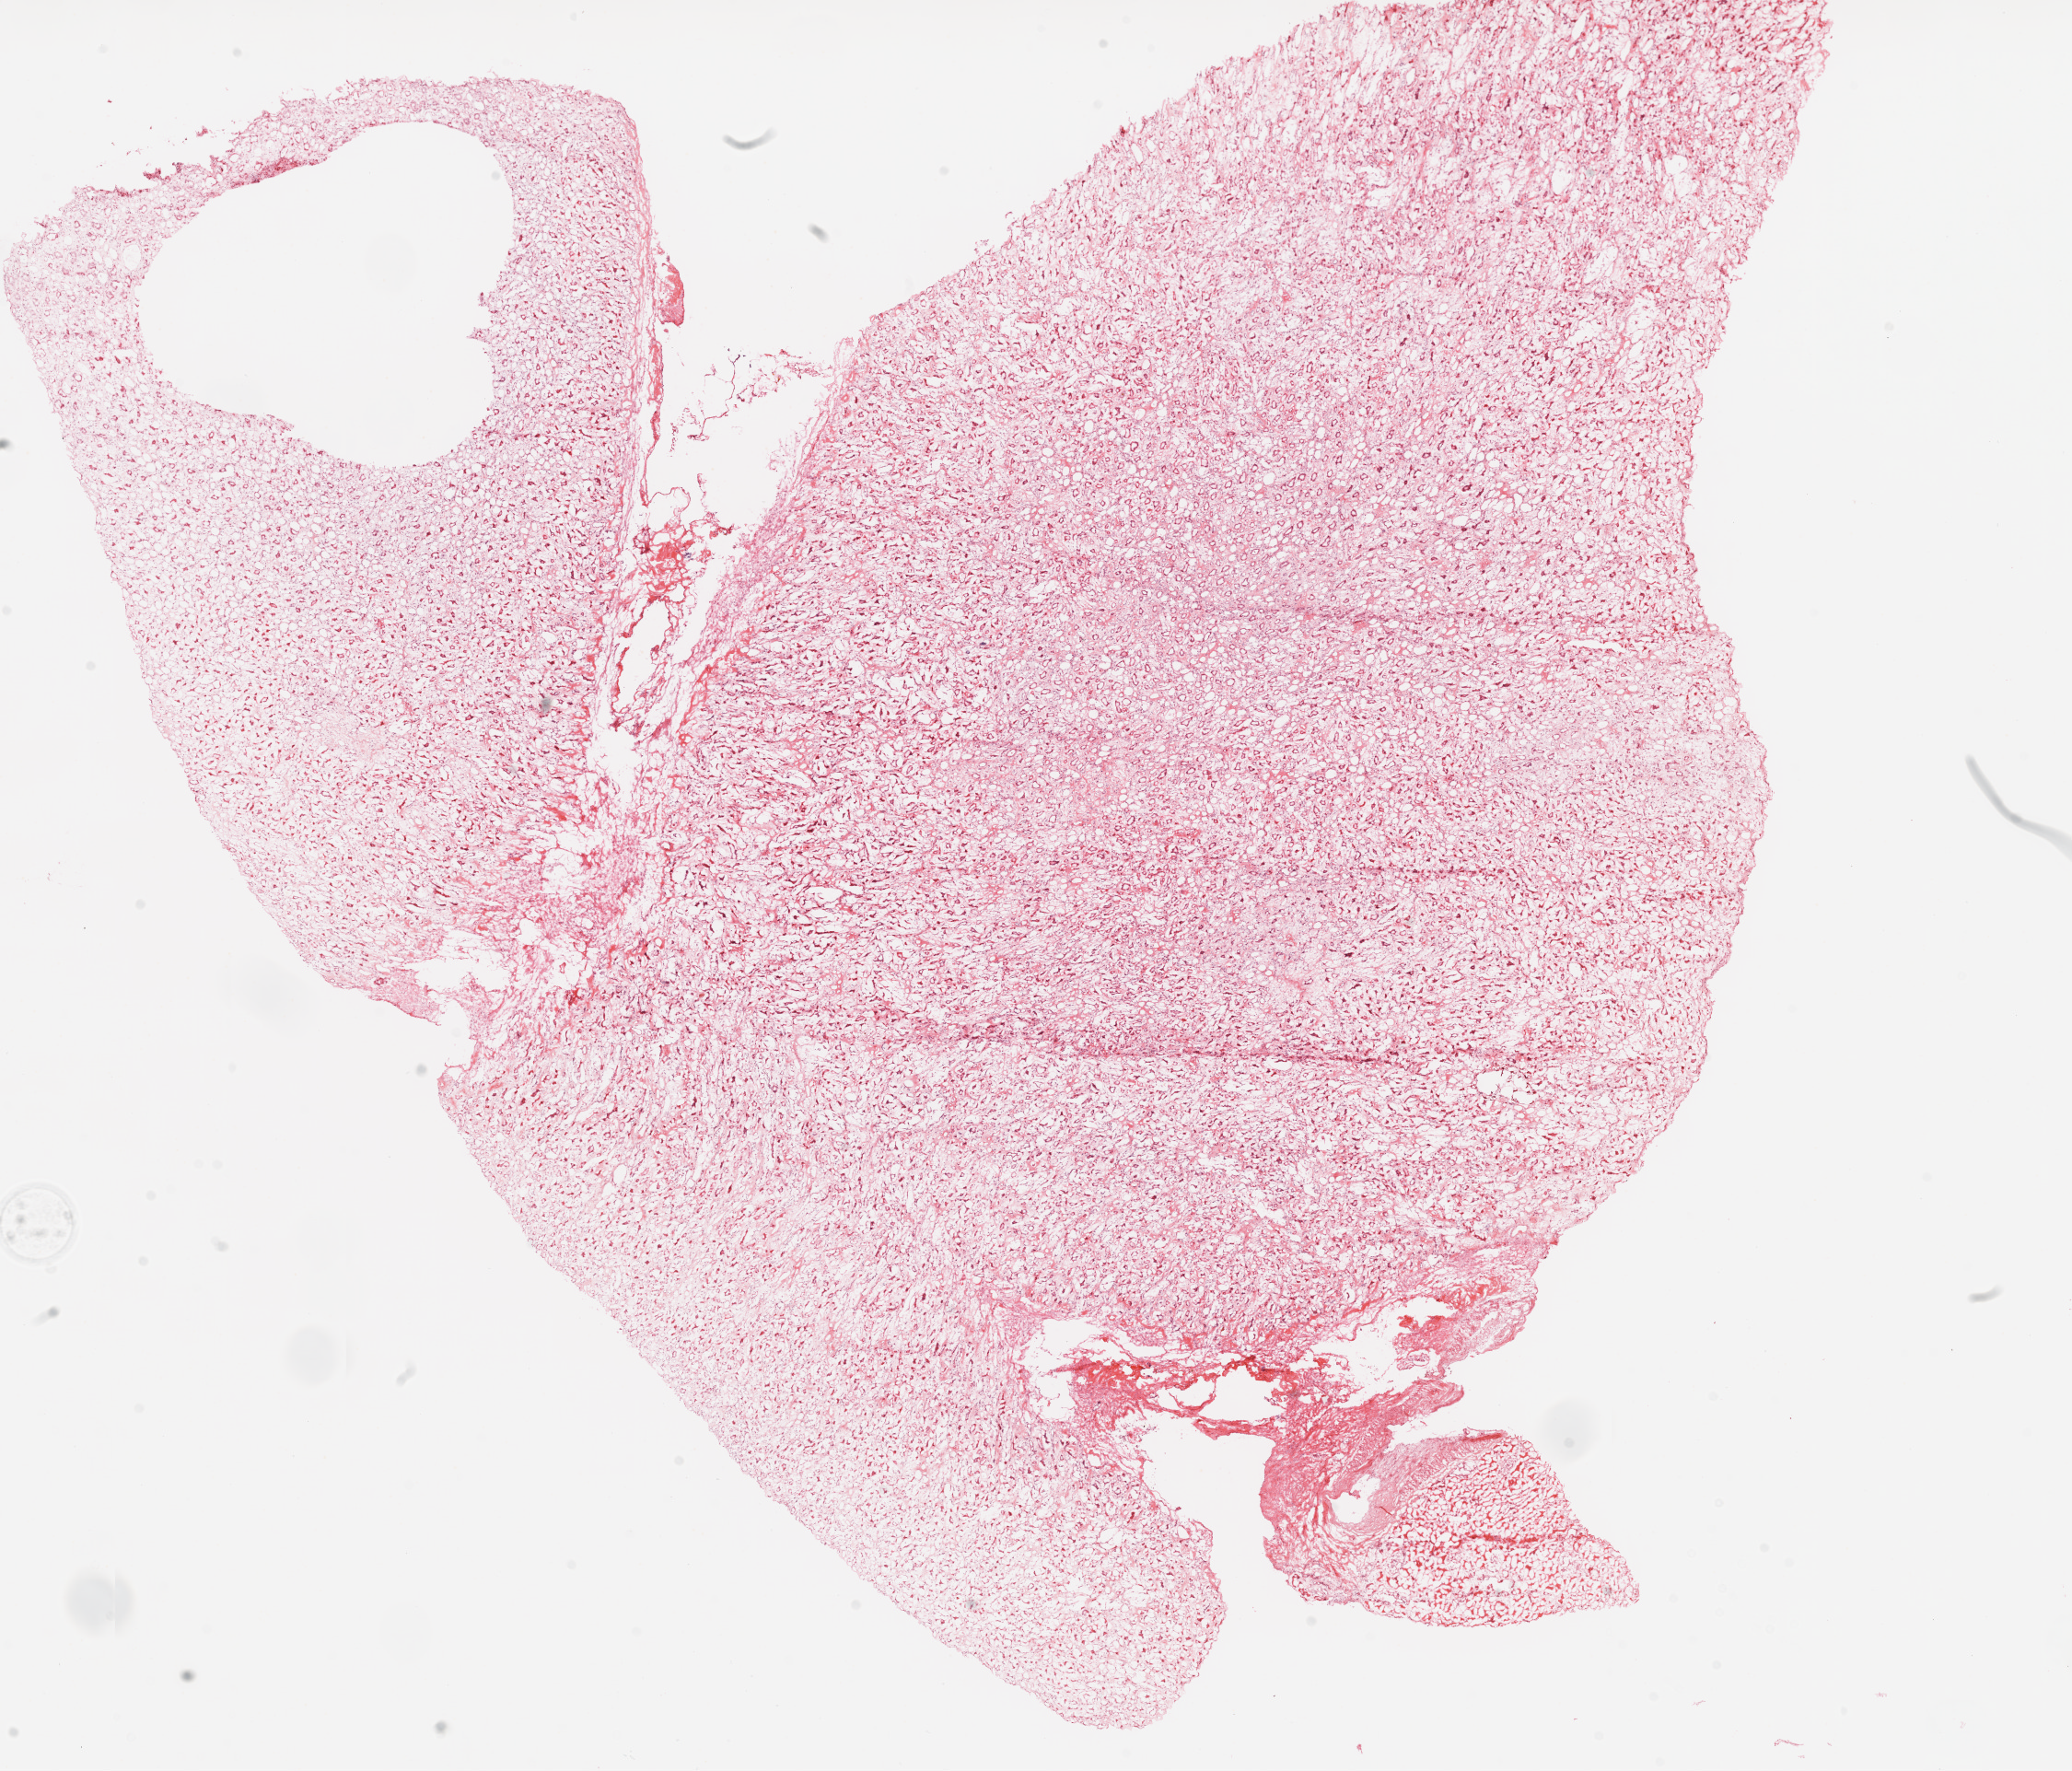
H&E-stained whole-slide image — whole scanned area (about 18.1 x 15.4 mm, slide scanned at 20x) shown as a low-resolution overview; frozen section from the top of the tissue portion; solid tissue normal (non-tumour tissue) sample from the kidney. Male patient; age at initial diagnosis 63 years.
• this section: solid tissue normal (non-tumour) sample from the same patient
• patient diagnosis: Clear cell adenocarcinoma, NOS